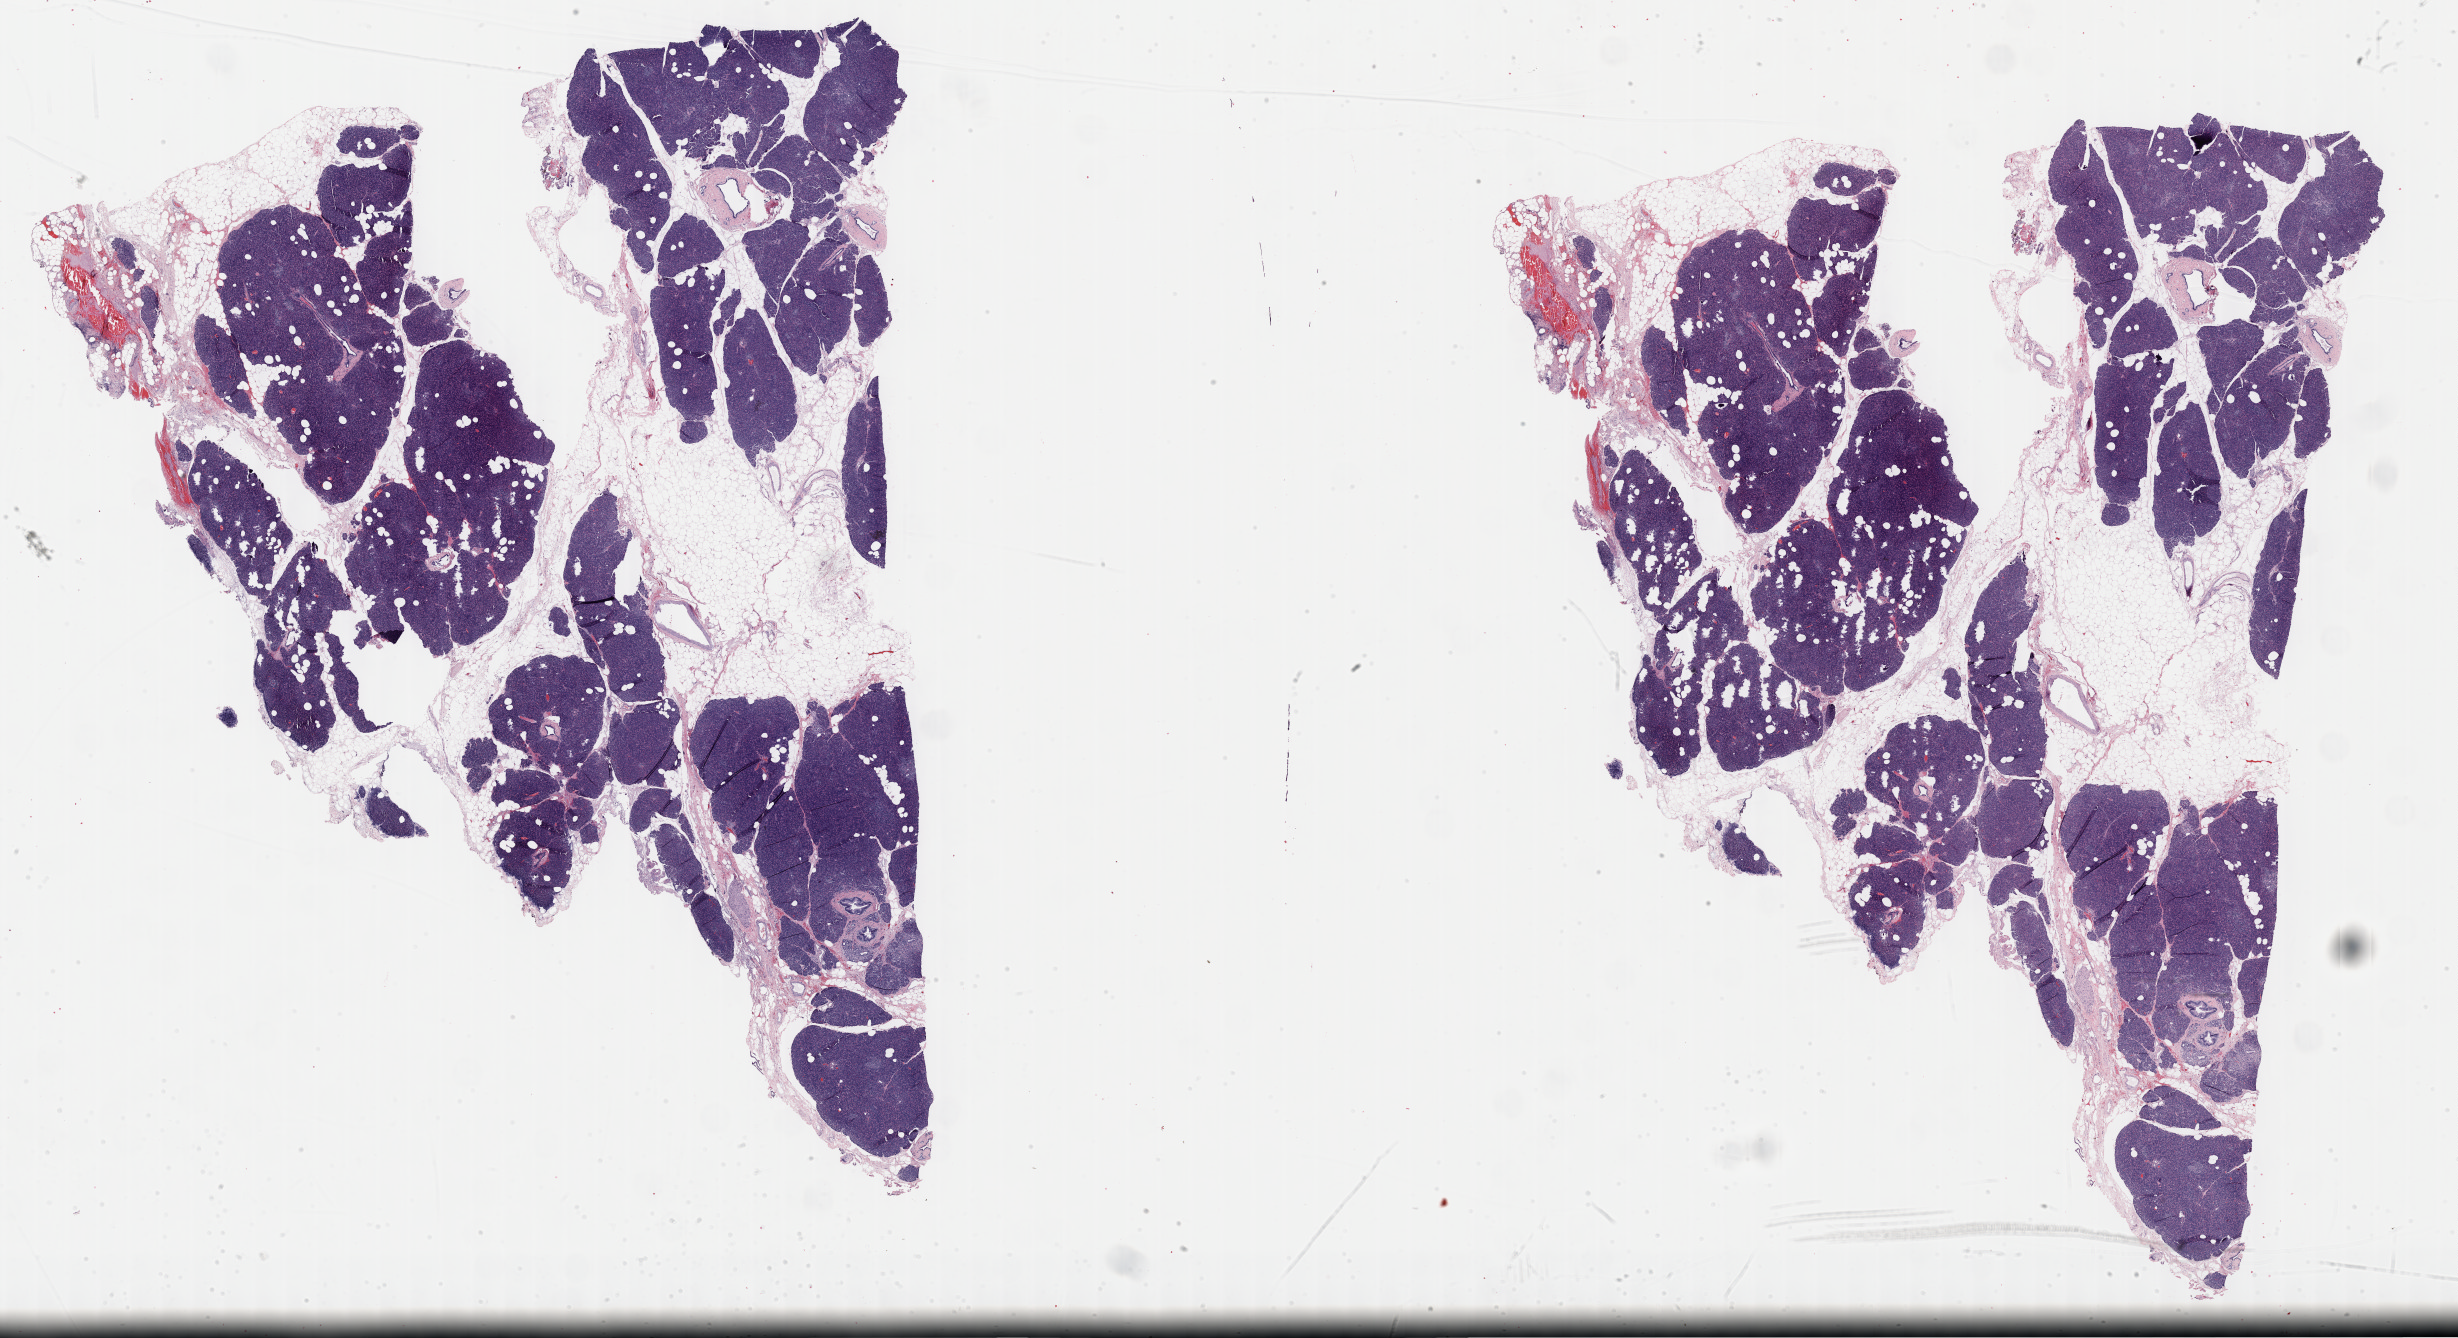
Hematoxylin and eosin (H&E) stained whole-slide image — whole scanned area (about 39.8 x 21.6 mm, acquisition: 40x scan) shown as a low-resolution overview; formalin-fixed paraffin-embedded (FFPE) diagnostic section; sample: primary tumour, pancreas. Female, age 48 years at initial diagnosis. Histologic grade: G3 (poorly differentiated).
• pathologic diagnosis: Infiltrating duct carcinoma, NOS (head of pancreas)
• lymph nodes positive (case pathology): 2 of 11 examined
• AJCC pathologic stage: IIB